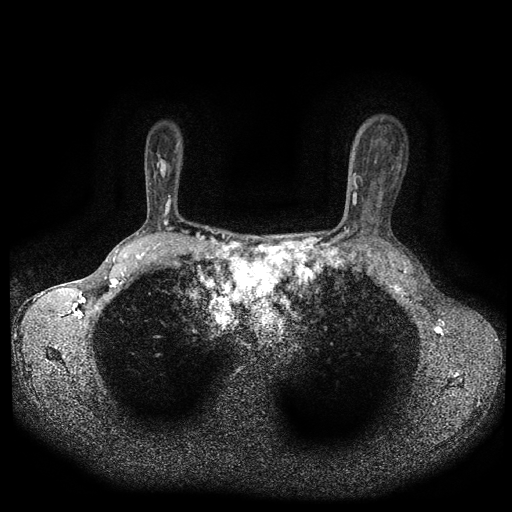
Breast MRI (dynamic contrast-enhanced, multi-phase), one axial slice. Position 74 of 116 along the scan axis. Dynamic contrast-enhanced series, time point 2 of 5 at this slice position (early post-contrast). 1.5 T. TE 2.7 ms, TR 5.4 ms. 2 mm slice thickness. 512 × 512 image matrix, field of view 330 × 330 mm. Patient: female, 49 years.
Annotated regions visible in this slice (semi-automatically segmented with operator editing):
- breast lesion (labelled benign in the annotation): bounding box [x1, y1, x2, y2] px = [155, 153, 168, 180]